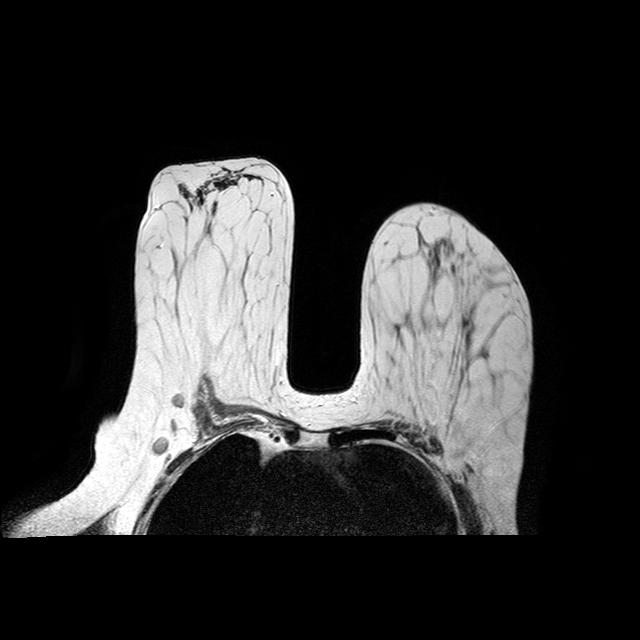
MRI of the breasts; 2 images, each one mid-volume slice chosen by position.
Image 1: axial T2-weighted / STIR image, slice 46 of 90, 2 mm slice thickness.
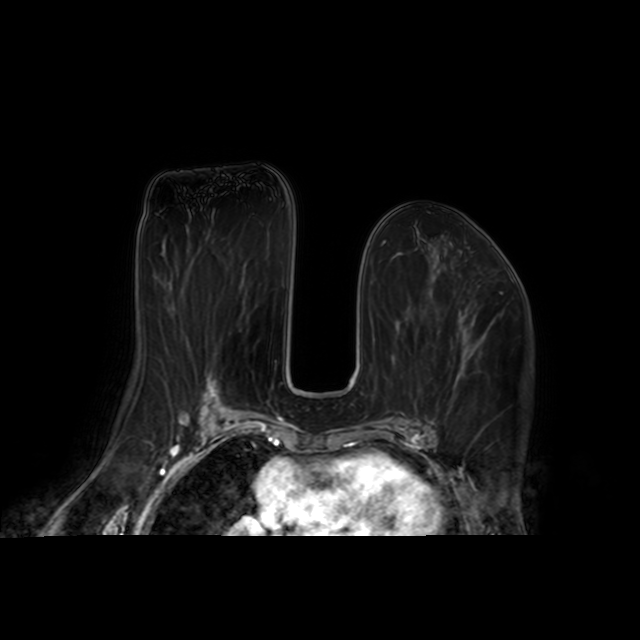
Image 2: axial dynamic contrast-enhanced T1-weighted image, series "AX BLISS_AUTO SENSE", slice 48 of 95, dynamic phase 5 of 8, 4 mm slice thickness.
Patient-level pathology facts (from the clinical record, not from the images): pathology diagnosis: ductal CA in situ (left breast); receptor status (as recorded): ER pos, PR pos, HER2 neg; pathology report notes: re-bx [date] at calcific shows no residual tumor.